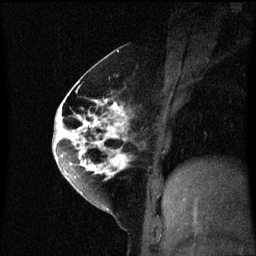
Breast MRI (dynamic contrast-enhanced), one sagittal slice; position 28 of 60 along the scan axis; dynamic contrast-enhanced series, image 2 of 3 at this slice position (ordered by acquisition); 1.5 T; TE 4.2 ms, TR 8.4 ms; 256 × 256 image matrix, field of view 200 × 200 mm. Patient: female, 60 years.
Outlined on this slice (semi-automatically segmented with operator editing):
- analysis volume of interest (the breast-tissue region the enhancement analysis was run in; not a lesion): bounding box [x1, y1, x2, y2] px = [64, 70, 133, 195]
- tumour enhancement mask (voxels above the 70 % enhancement threshold inside the analysis volume of interest): [64, 78, 131, 191]